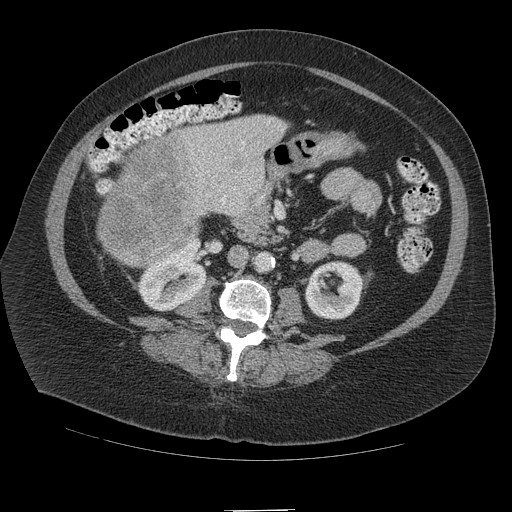
Contrast-enhanced abdominal CT (liver protocol), one axial slice. Slice 34 of 109 in the series (ordered by position). Soft-tissue window (W 400 / L 40 HU). 512 × 512 image matrix, field of view 420 × 420 mm. From the clinical record (not read from this slice): diagnosis: hepatocellular carcinoma (patient treated with transarterial chemoembolisation; whether this scan precedes or follows treatment is not stated here); TNM stage (as recorded): Stage-IVB; Child-Pugh class: A; tumour differentiation: poorly differentiated; tumour nodularity: multinodular.
Structures marked on this image (semi-automatic segmentation, software-assisted and operator-edited):
- liver parenchyma outside the tumour (the mass and vessels are separate outlines, so this box may not span the whole liver): bounding box (x1, y1, x2, y2) in pixels: (114, 114, 286, 232)
- mass: (97, 135, 203, 266)
- liver vessels: (192, 141, 245, 205)